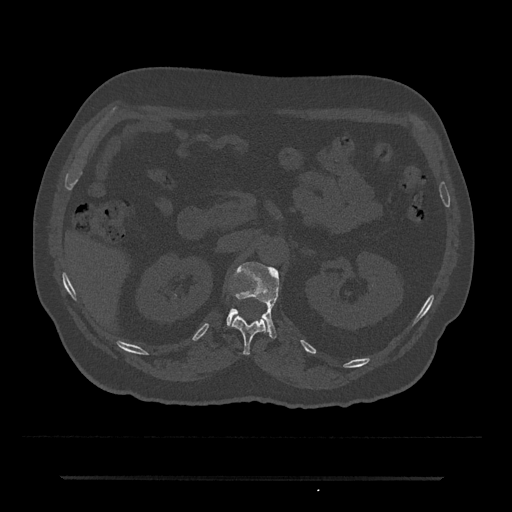
CT including the spine, one axial slice; slice 102 of 797 in the series (ordered by position); reconstruction kernel Br40s/3; 120 kVp; bone window (W 1800 / L 400 HU); 512 × 512 image matrix, field of view 437 × 437 mm. Male patient, age 69 years. Case-level facts recorded for this patient, not image findings: primary cancer: prostate.
Annotated regions visible in this slice (semi-automatic segmentation, software-assisted and operator-edited):
- L1 vertebra: box from (x=227, y=262) to (x=279, y=338) px
- T12 vertebra: (x=232, y=313)–(x=268, y=355)